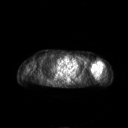
FDG PET of an extremity soft-tissue mass (from a PET/CT study), one axial slice; slice 172 of 267 in the series (ordered by position); 128 × 128 image matrix. Patient: female, 83 years. Case-level facts recorded for this patient, not image findings: histological type: pleiomorphic leiomyosarcoma; grade: high; site of the primary tumour: left biceps.
Annotated regions visible in this slice (expert contour drawn on MRI and transferred to this co-registered scan by the dataset authors):
- gross tumour volume including surrounding oedema: box from (x=90, y=59) to (x=104, y=77) px
- gross tumour volume (mass): (x=90, y=59)–(x=103, y=76)